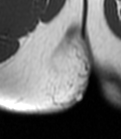
MRI of an extremity soft-tissue mass, one axial slice; slice 11 of 47 in the series (ordered by position); MR volume resampled by the dataset authors to the PET/CT grid (not the native acquisition matrix); 3.27 mm slice thickness; 121 × 139 image matrix, field of view 118 × 136 mm. Female patient. From the clinical record (not read from this slice): histological type: epithelioid sarcoma; grade: intermediate; site of the primary tumour: right buttock.
Outlined on this slice (expert contour drawn on MRI and transferred to this co-registered scan by the dataset authors):
- gross tumour volume including surrounding oedema: box from (x=50, y=59) to (x=80, y=99) px